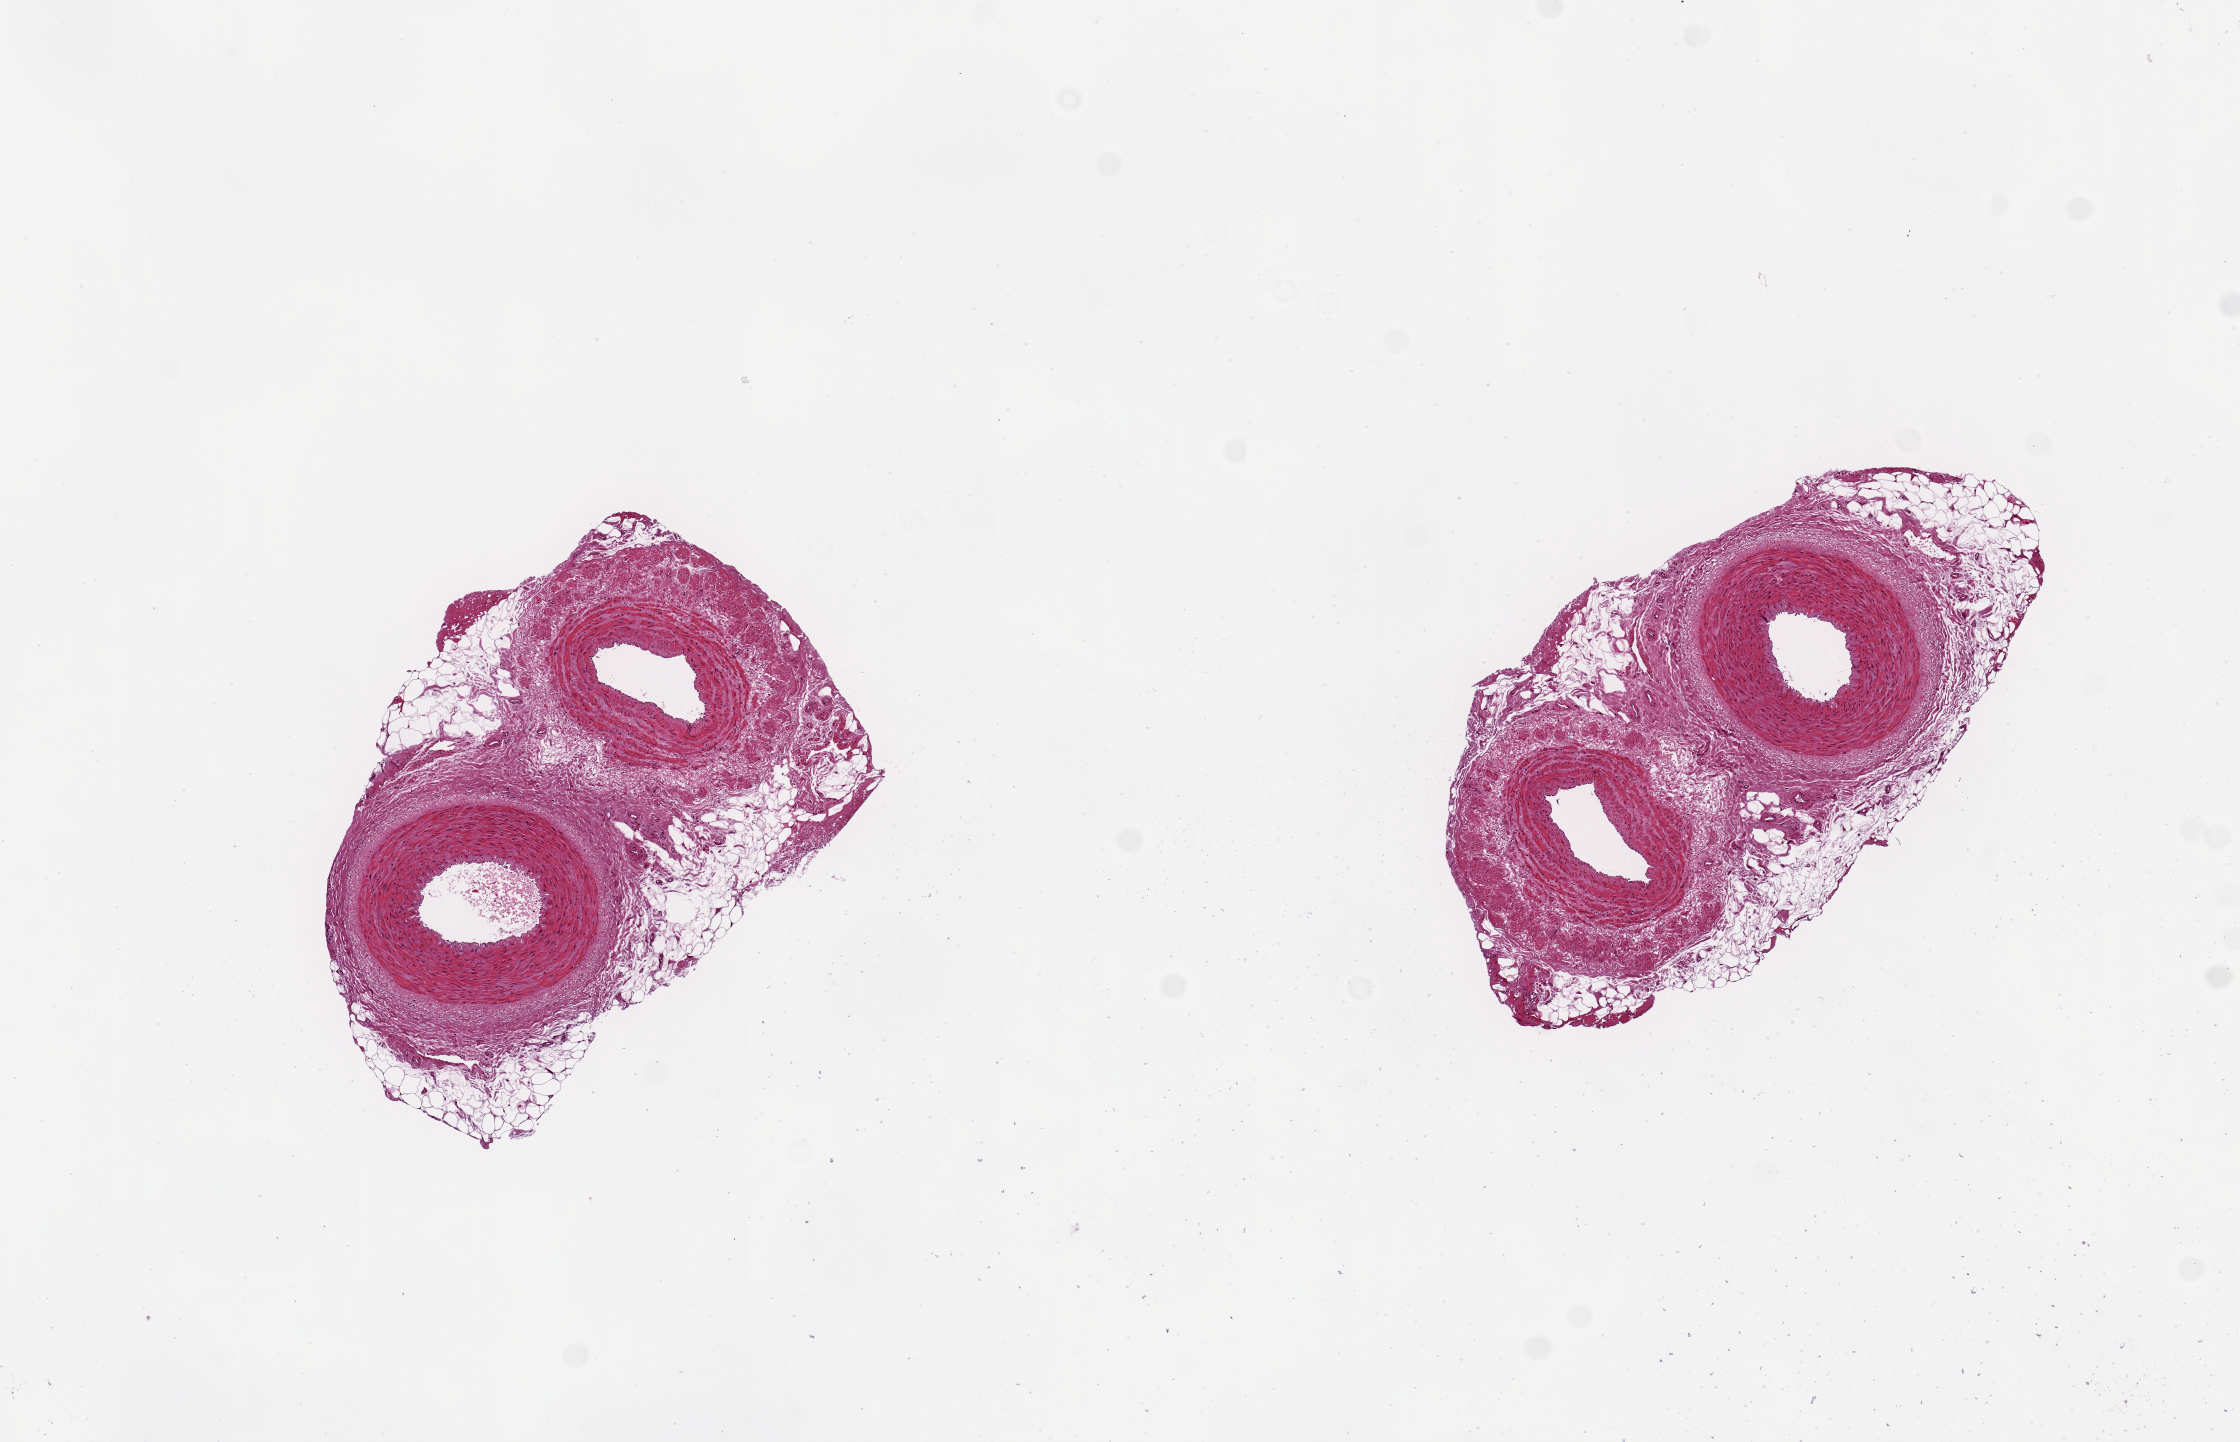
Whole-slide image, hematoxylin and eosin (H&E) stain — low-resolution overview of the scanned area, about 8.9 x 5.7 mm, PAXgene-fixed paraffin-embedded (PFPE) section, section of tibial artery (target tissue), tissue donor sample. Male donor.
Review note (as recorded): 2 pieces each with 1mm artery and 0.8 mm vein plus ~30% of each 2.5 mm aliquot with surrounding fat and stroma.